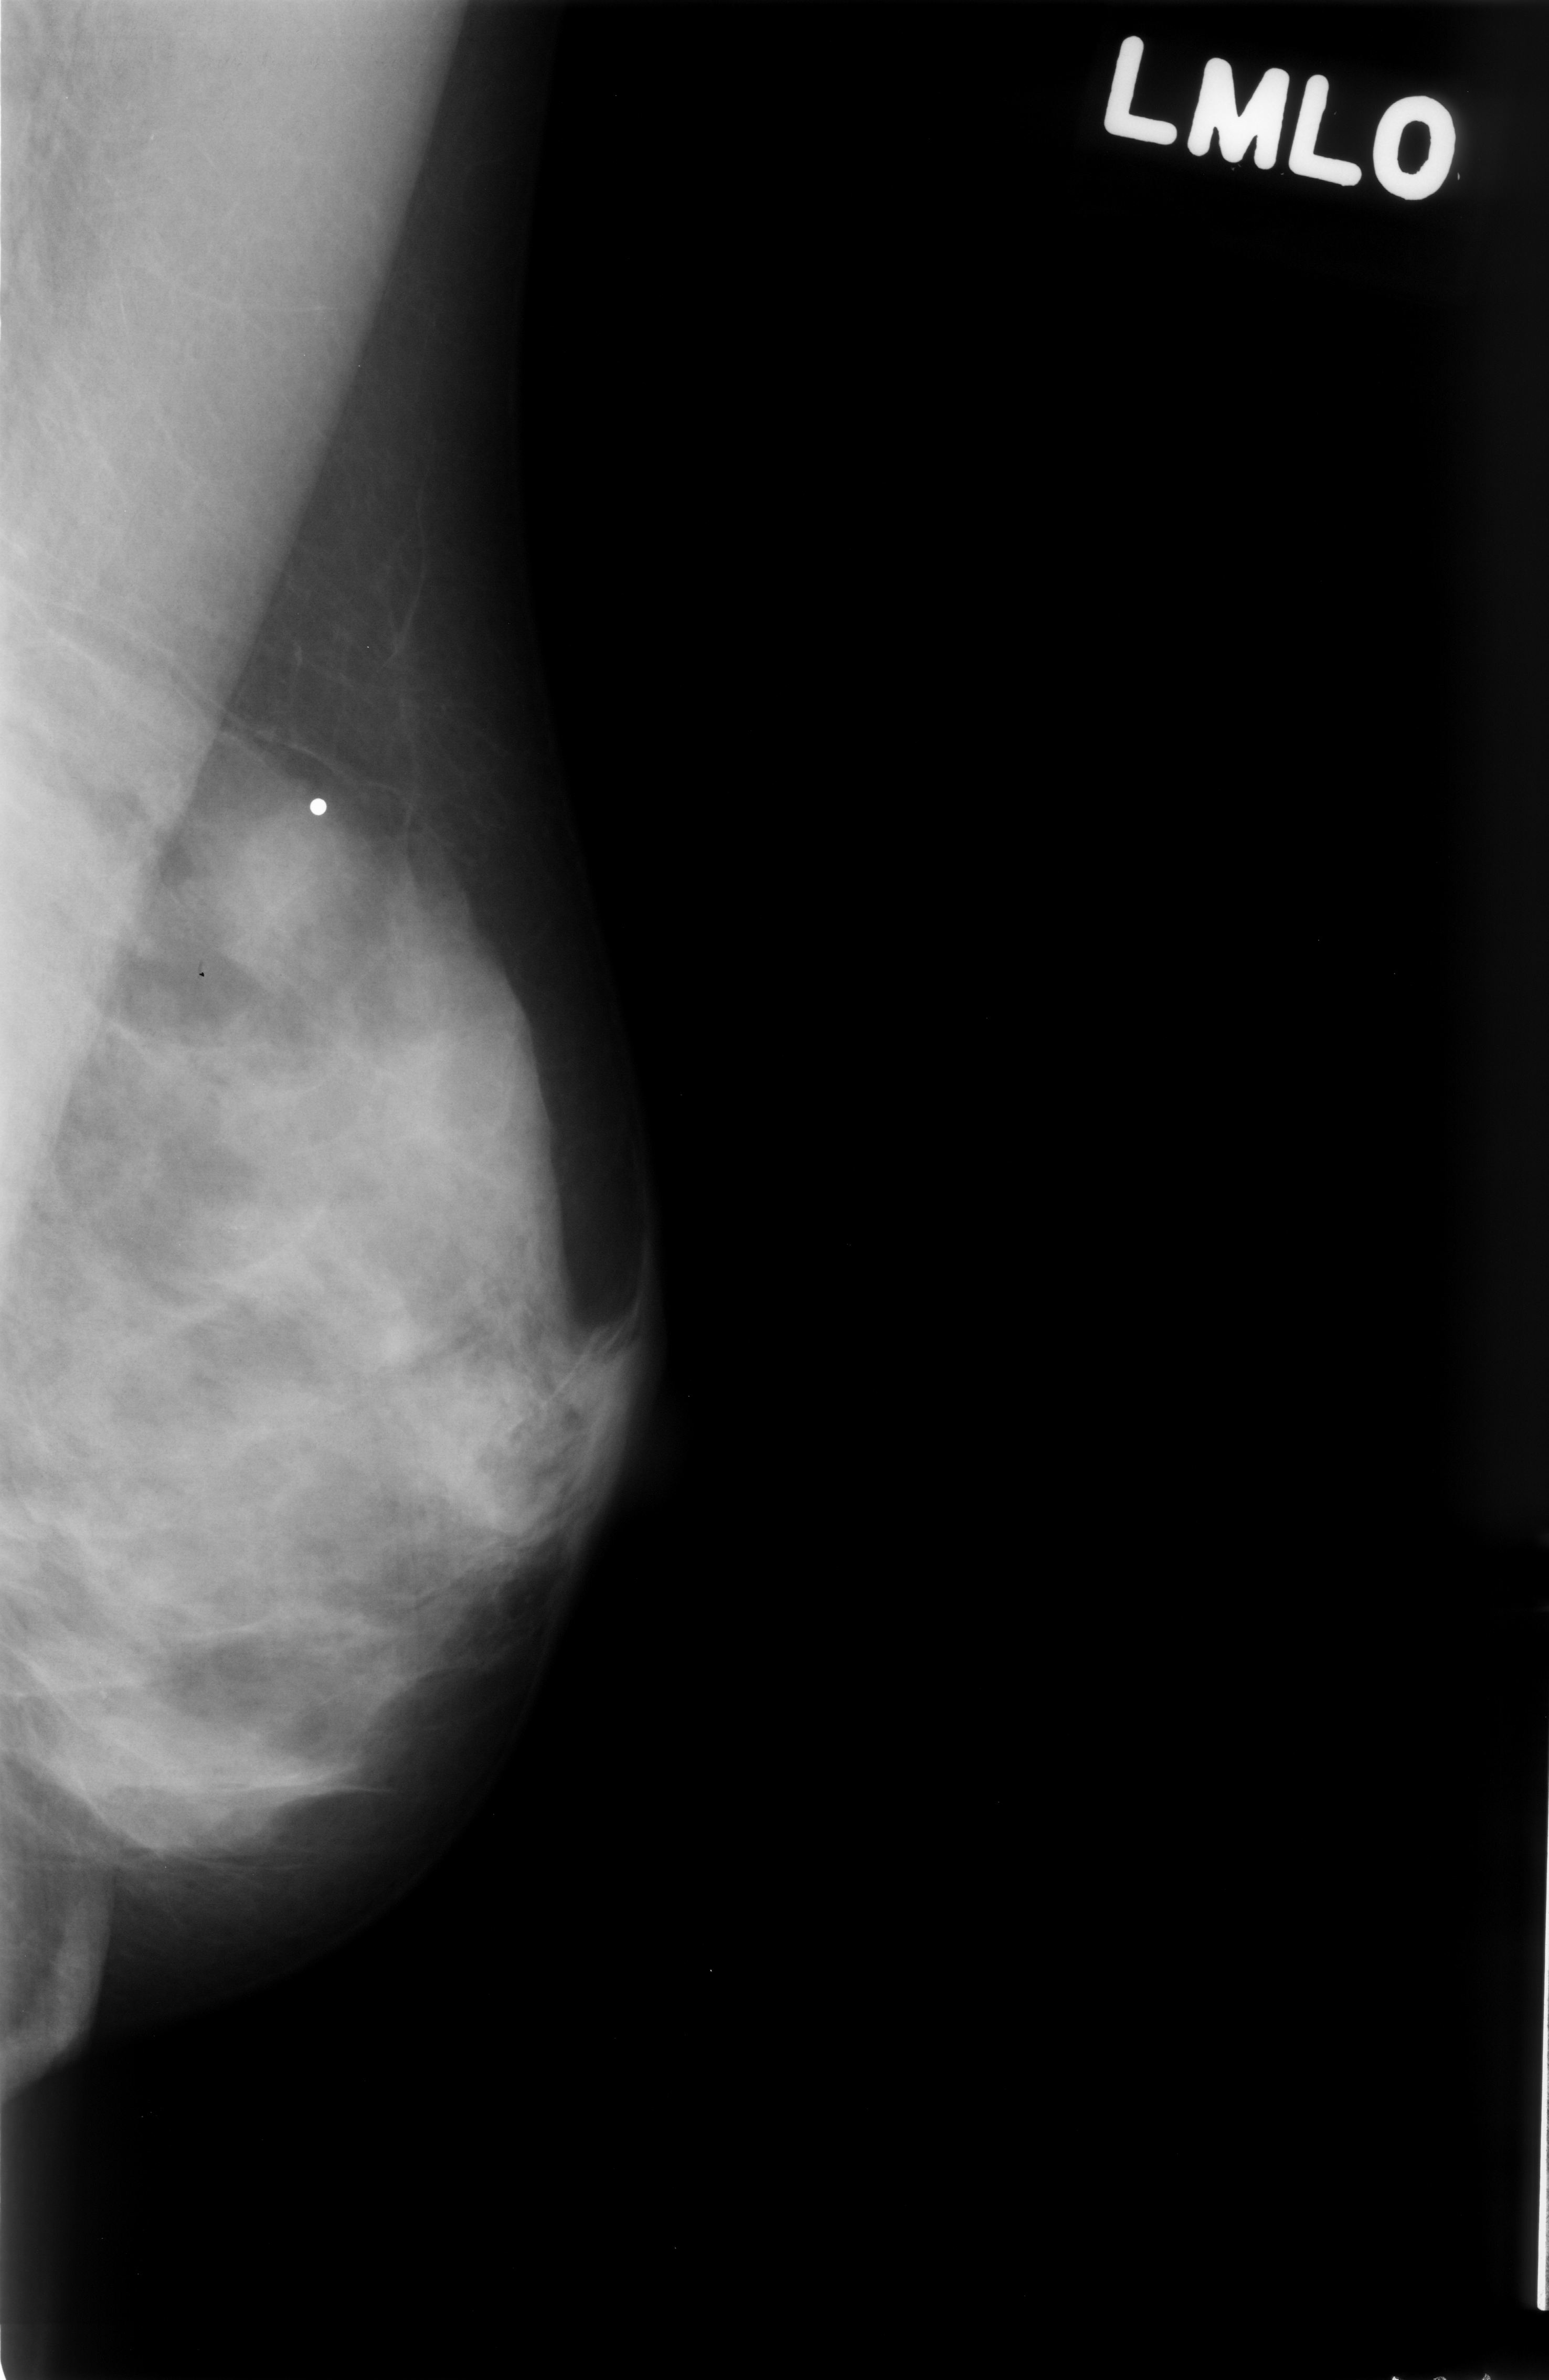
Digitized screen-film mammogram, left breast, mediolateral oblique (MLO) view.
Abnormality record for this image: calcifications, morphology amorphous, distribution clustered; BI-RADS assessment category 4; subtlety rating 2 on a 1 (subtle) to 5 (obvious) scale; pathology result (as recorded, not read from the image): benign.